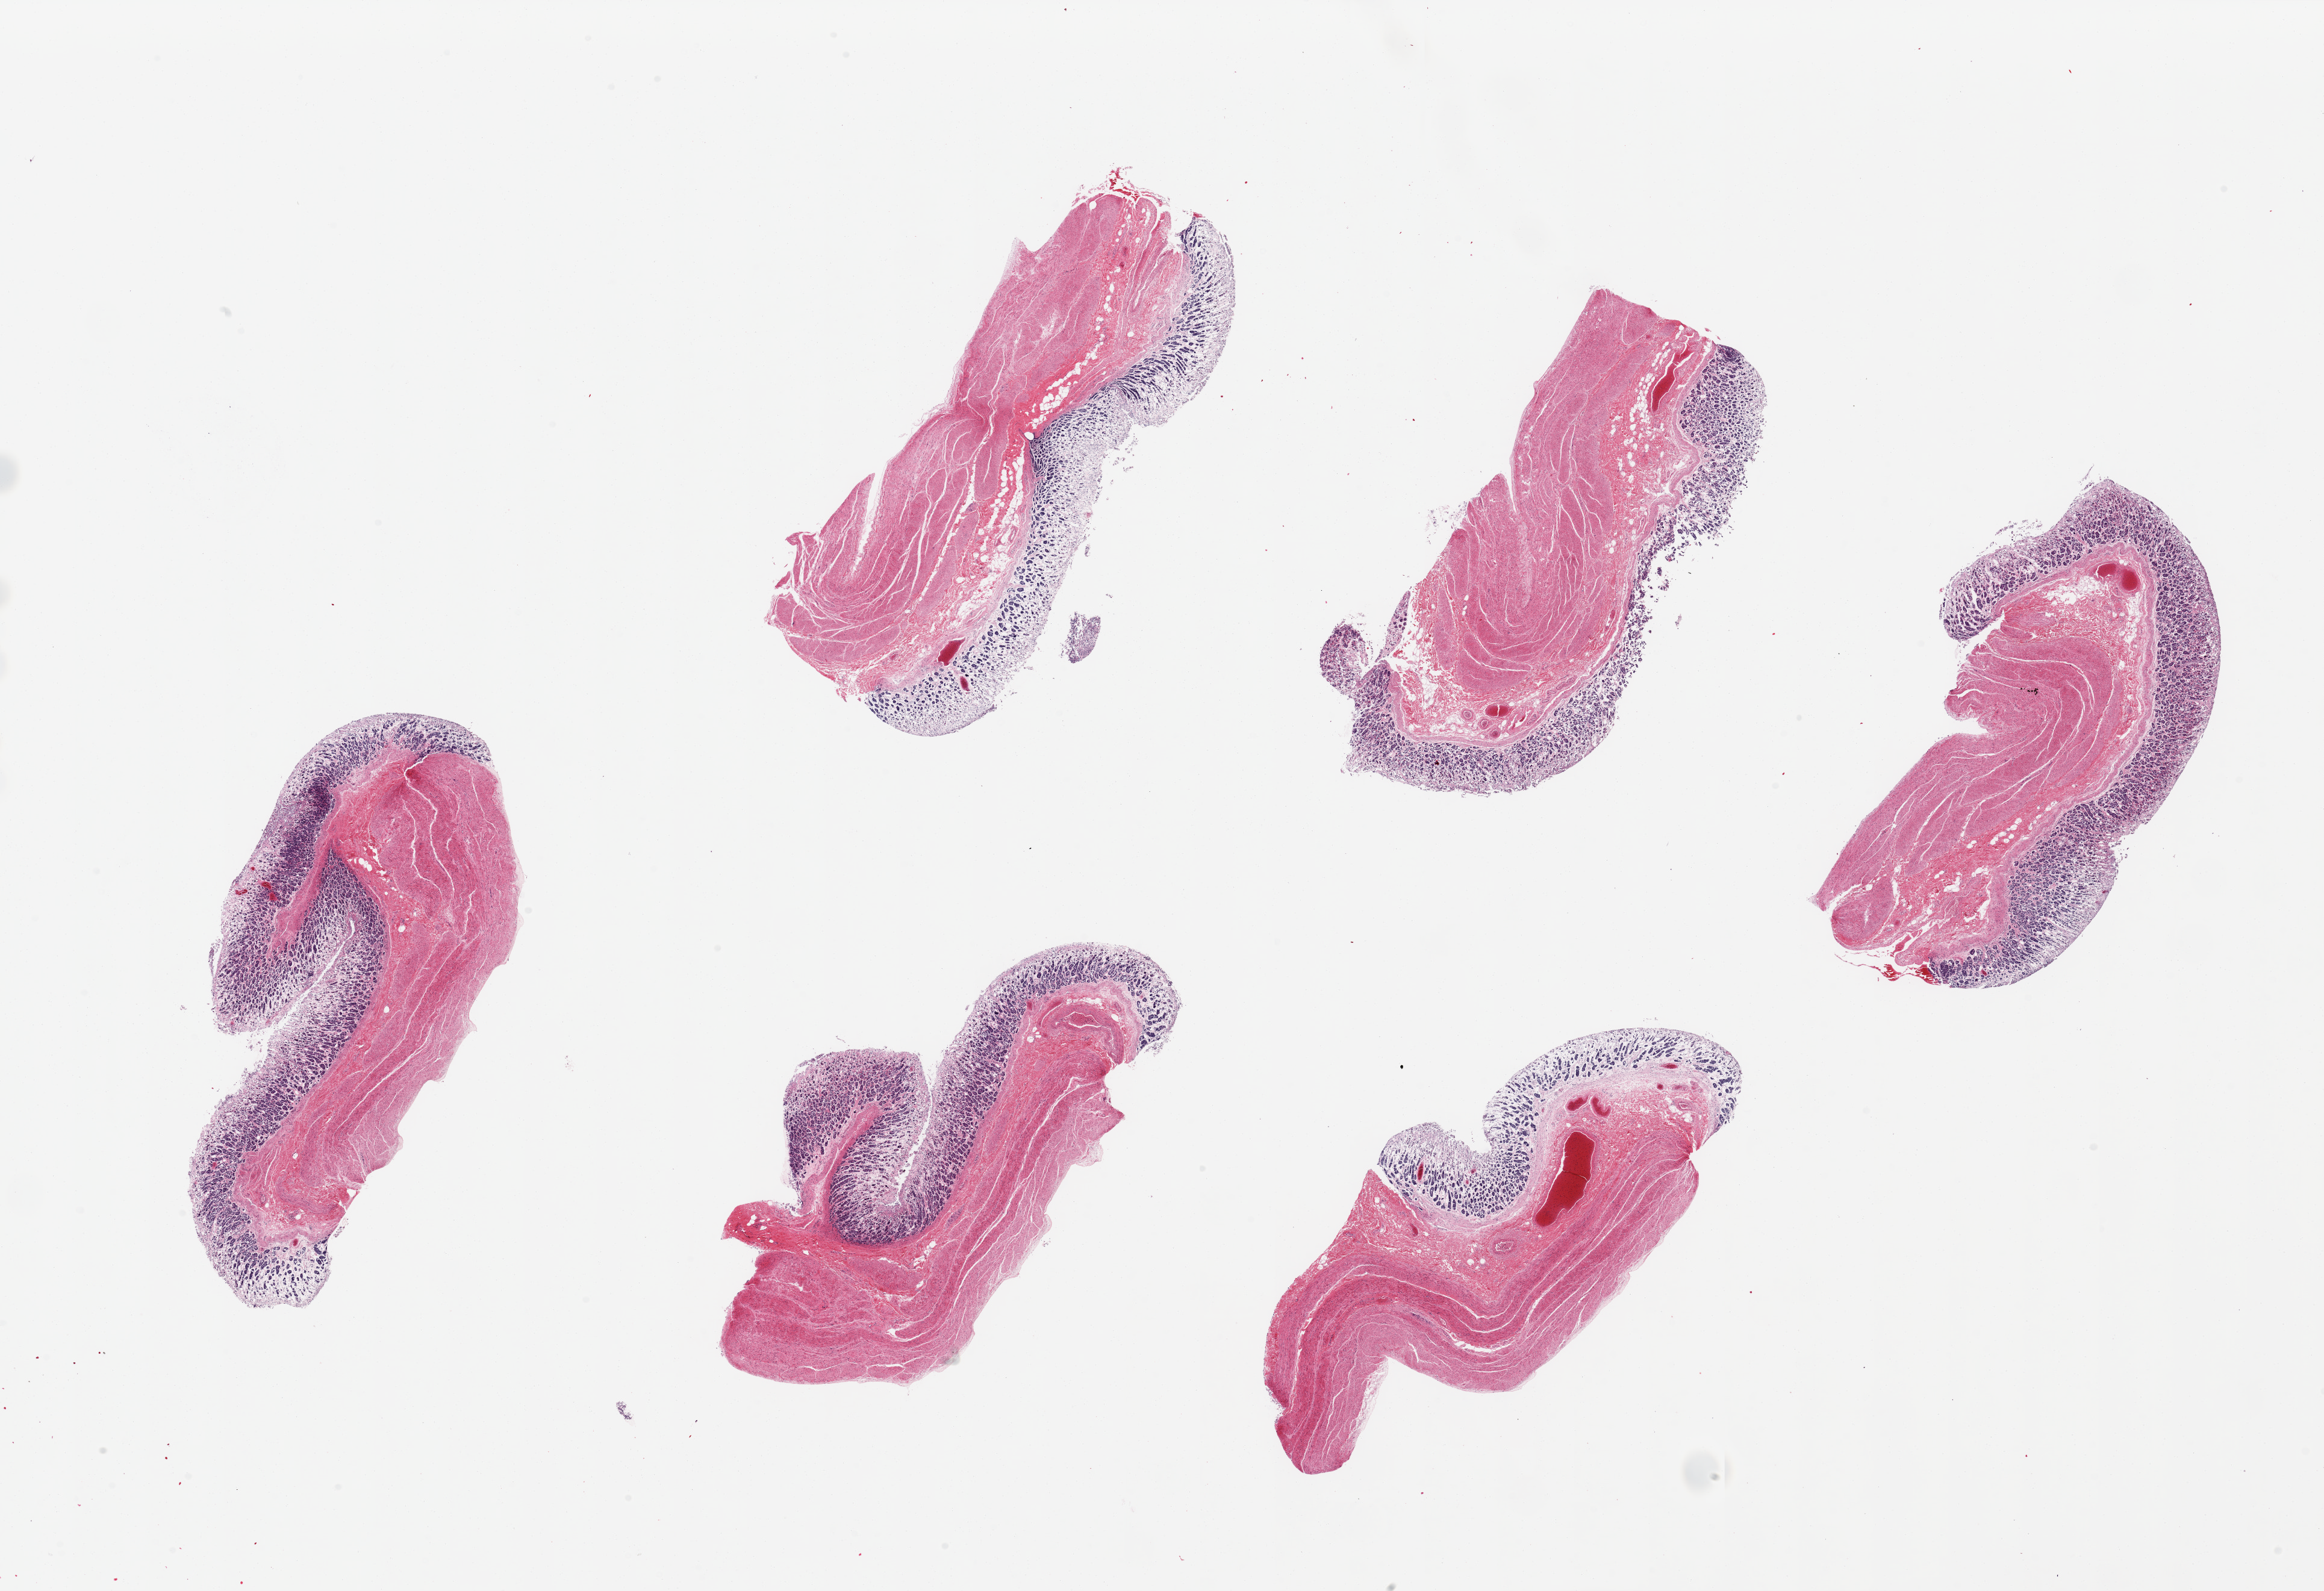
Whole-slide image, H&E stain — low-resolution overview of the scanned area, about 30.5 x 20.9 mm (slide scanned at 20x). PAXgene-fixed, paraffin-embedded tissue. Section of stomach (target tissue). Donor tissue sample. Male donor.
Pathologist's review note for this sample: 6 pieces ~7x3mm, mucosa totally autolyzed.